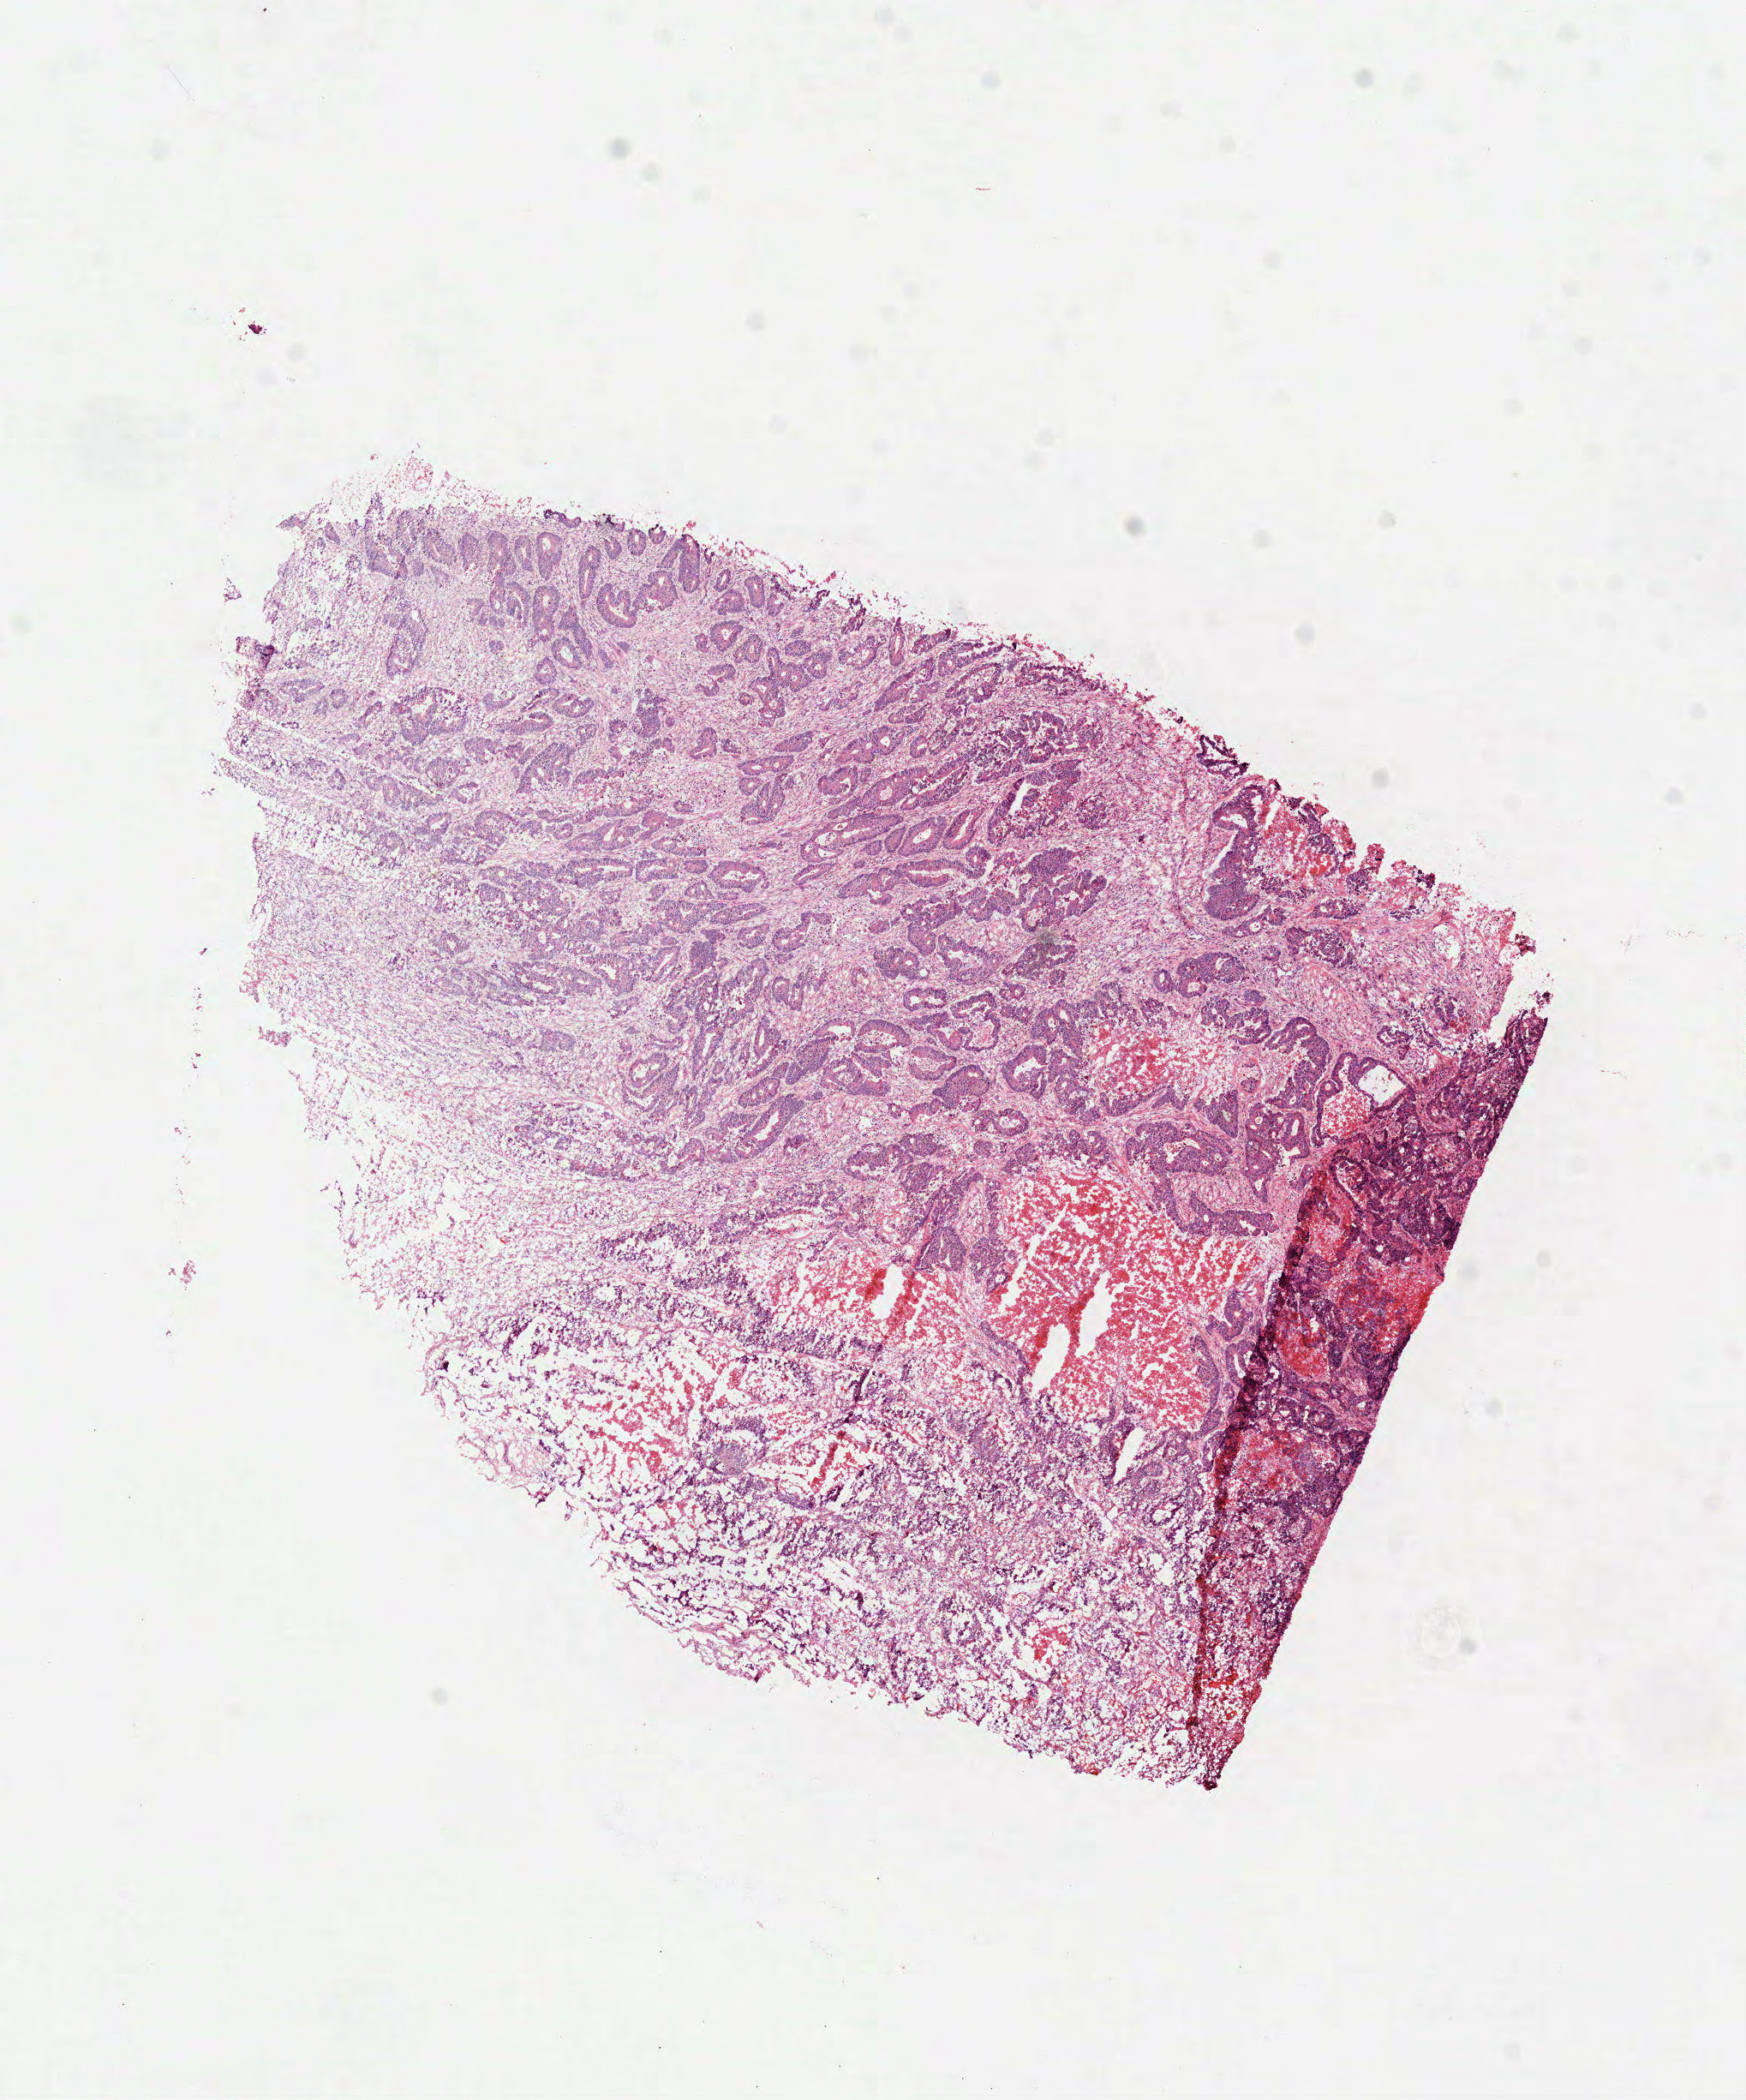
Whole-slide histology image, Hematoxylin and eosin (H&E) stained — whole scanned area (about 8.2 x 9.9 mm, slide scanned at 40x) shown as a low-resolution overview, frozen section from the top of the tissue portion, primary tumour sample from the colon. Patient: male, age at initial diagnosis 69 years. Pathologist review of this section (percent, as recorded): tumour cells 60%, tumour nuclei 75%, normal cells 0%, stromal cells 35%, necrosis 5%. Inflammatory infiltration, as recorded: lymphocyte infiltration 1%, monocyte infiltration 0%, neutrophil infiltration 1%.
Histologic diagnosis: Adenocarcinoma, NOS. TNM: T3 N0 M0. AJCC pathologic stage: IIA (7th edition).